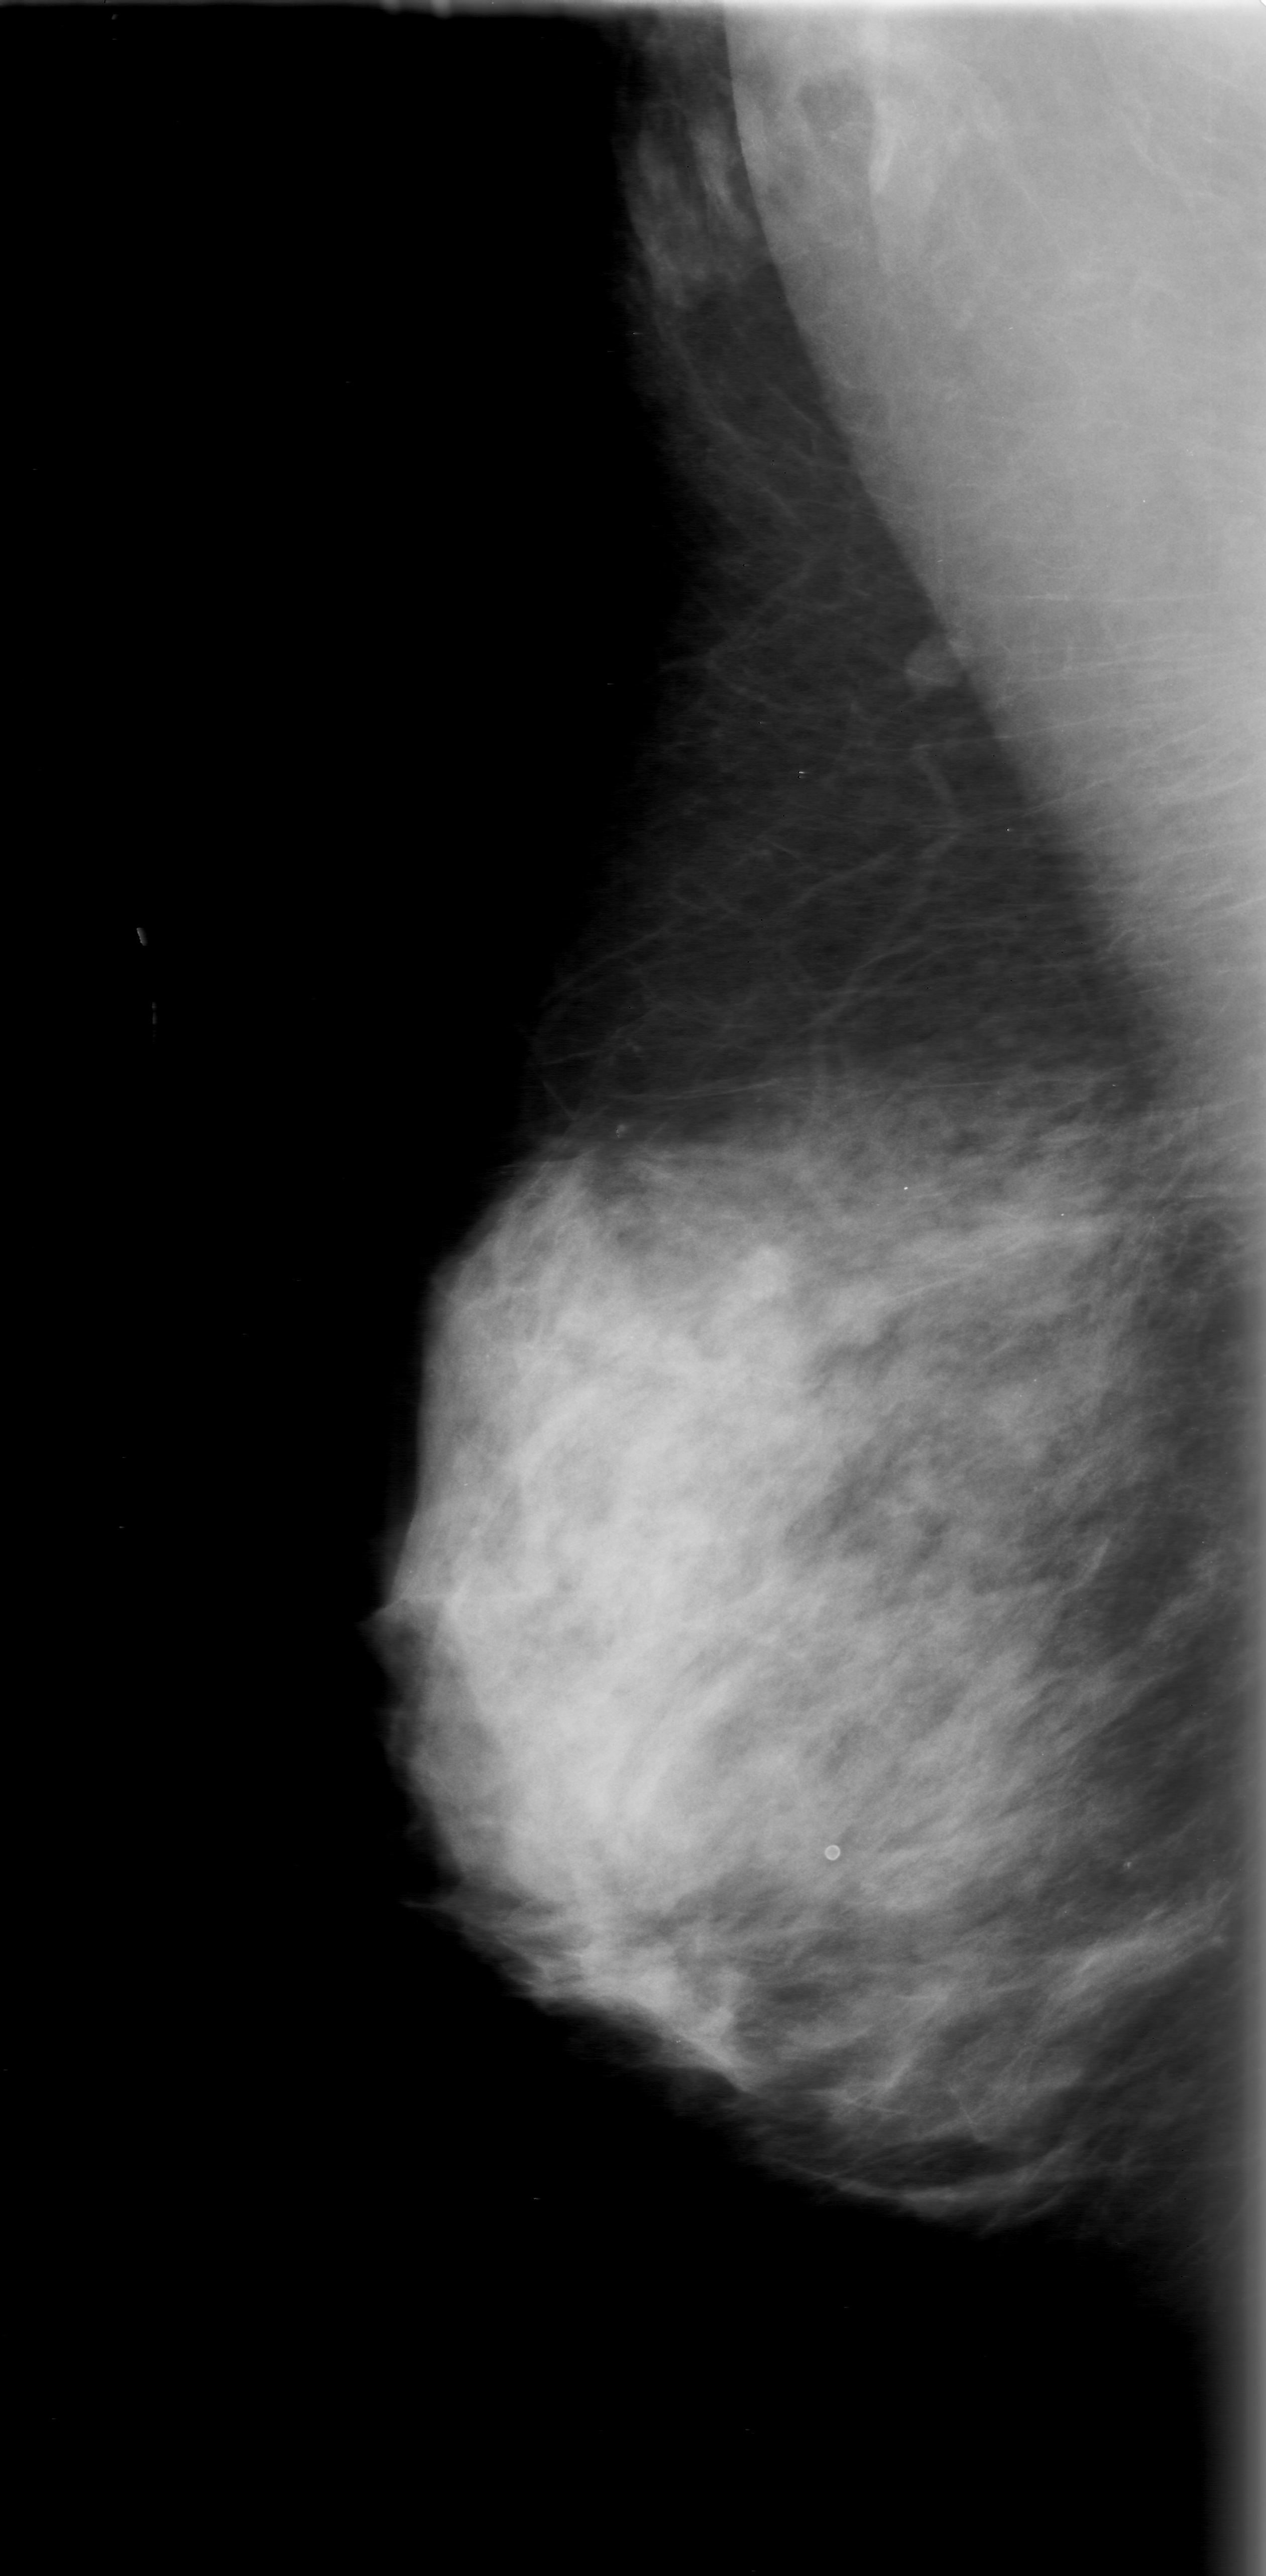
Scanned film-screen mammogram. Right breast. Mediolateral oblique (MLO) view. BI-RADS breast density category 4 (scale 1–4). 1266 × 2576 image matrix.
Marked abnormalities (boxes around the expert regions of interest):
- mass, shape lobulated, margins obscured; BI-RADS assessment category 0 (incomplete: needs additional imaging); pathology (as recorded): benign: box from (x=581, y=1940) to (x=695, y=2026) px